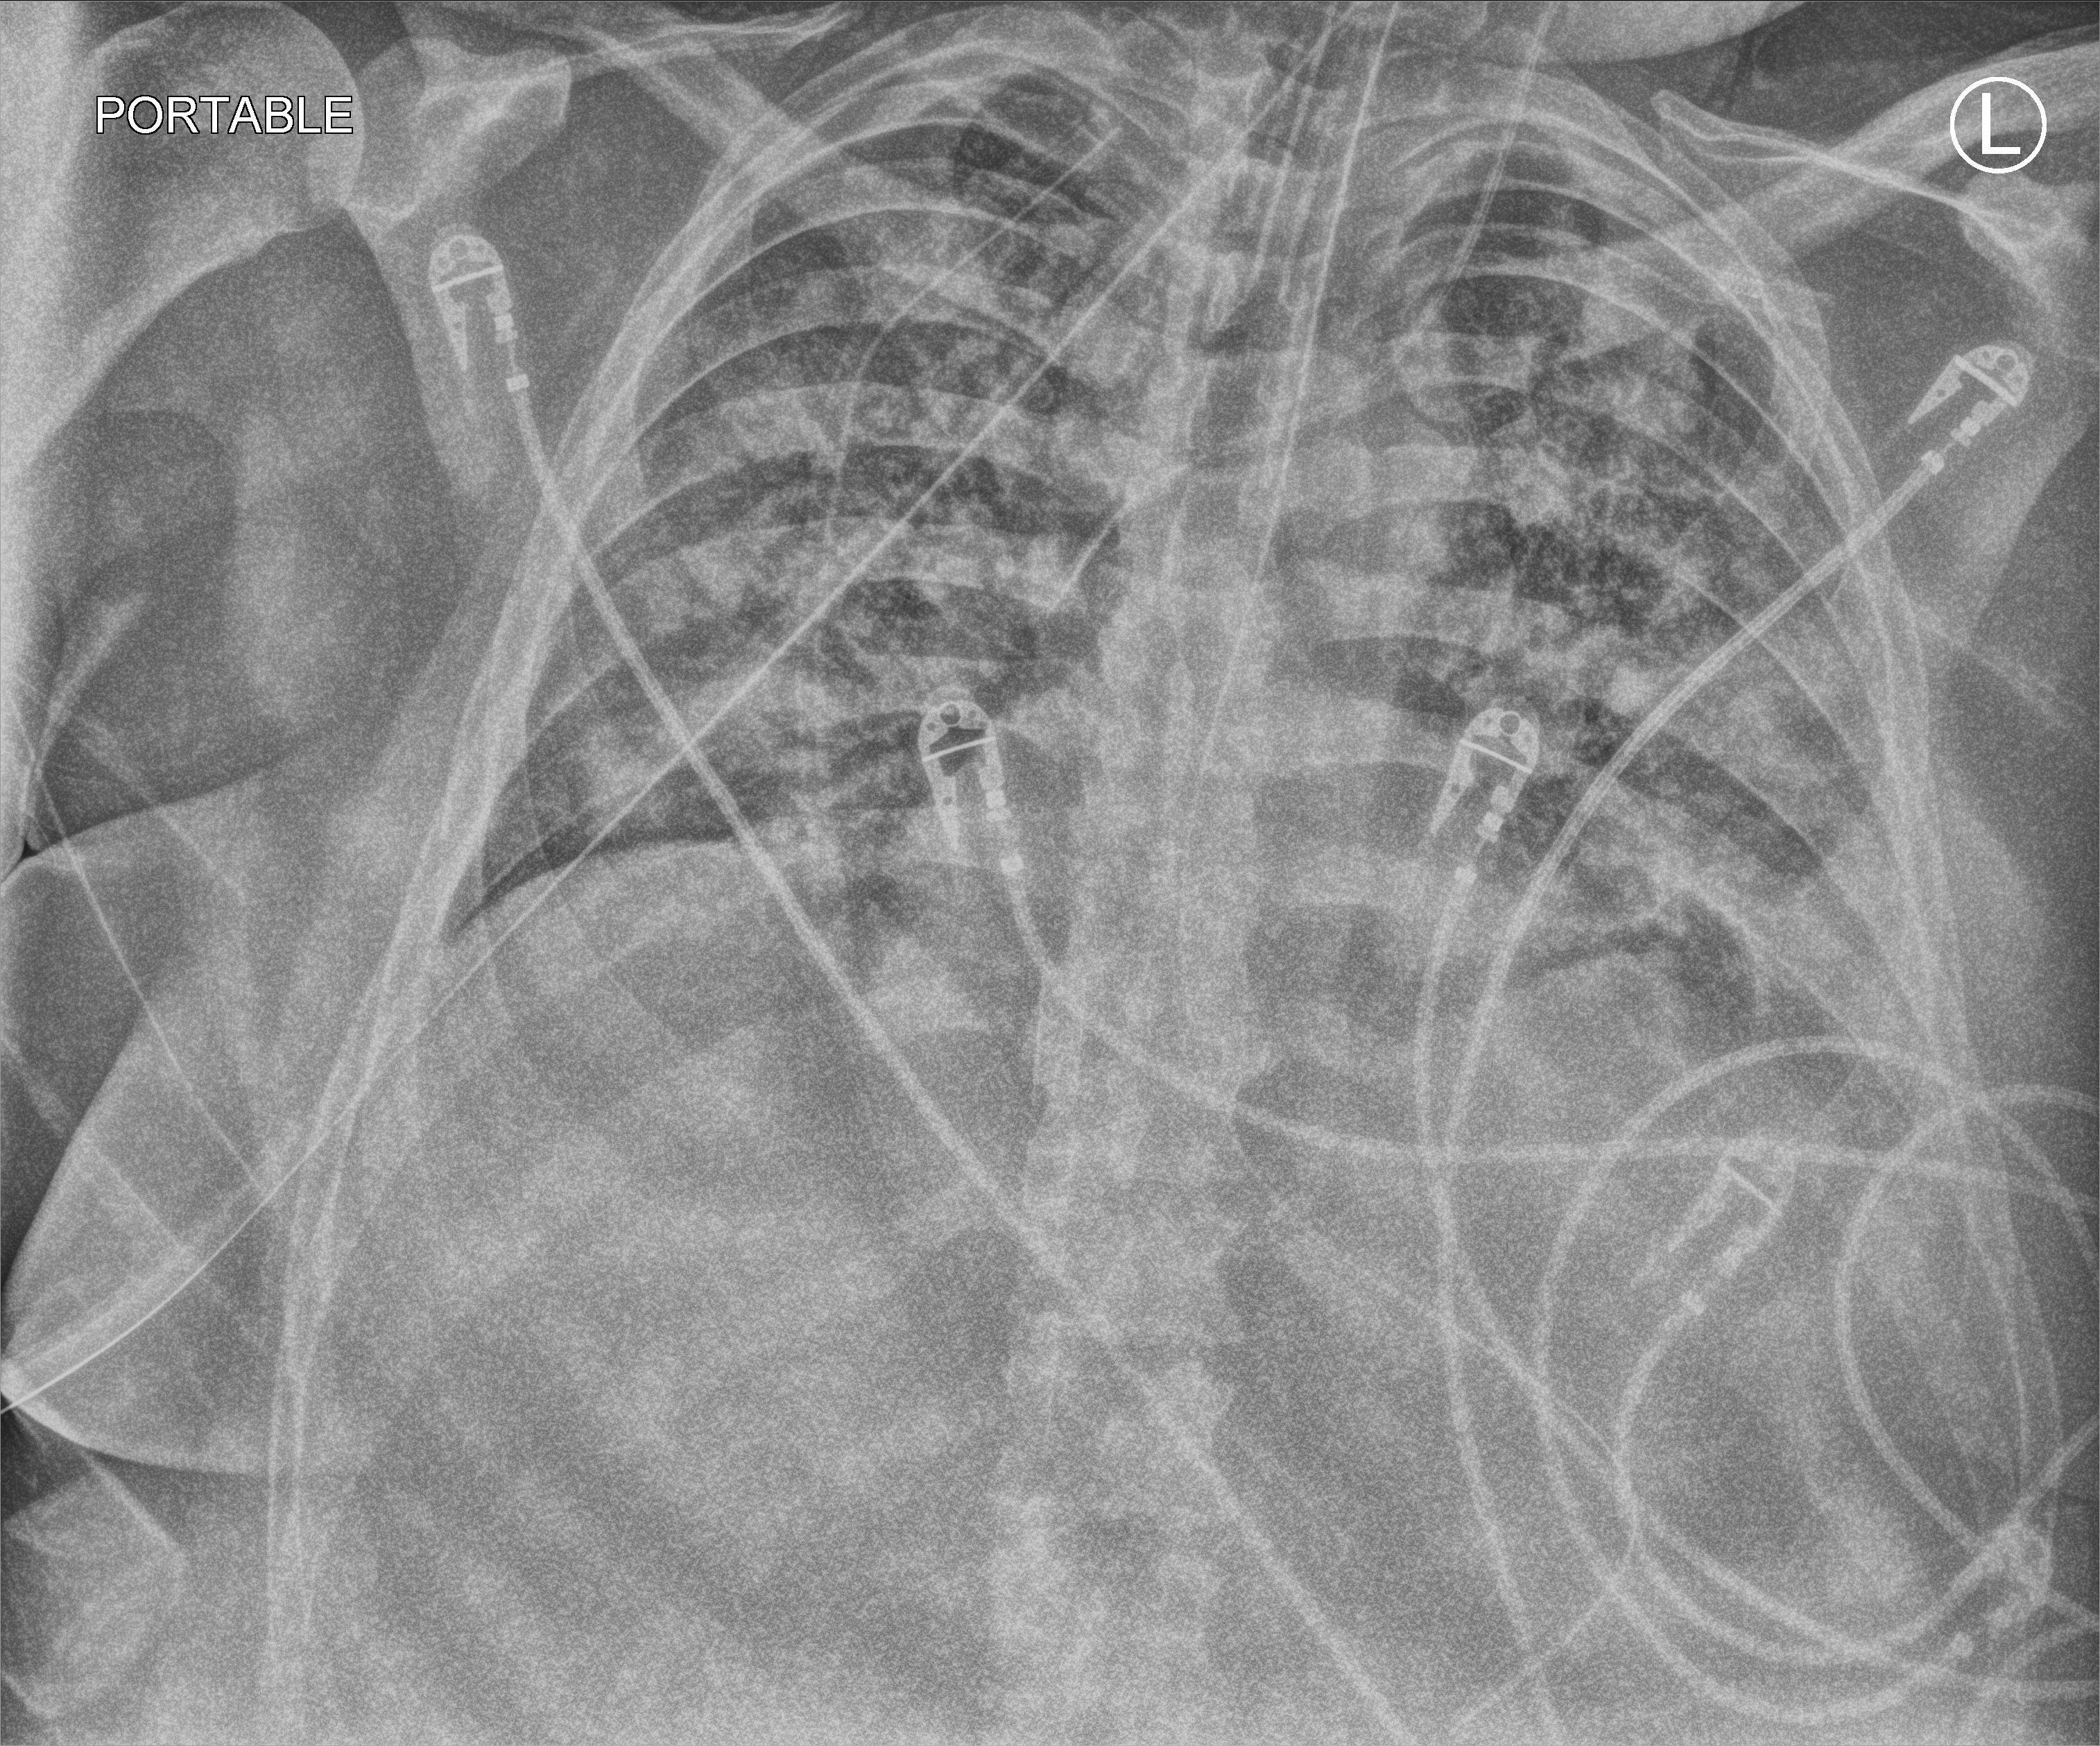
Chest X-ray (portable); anteroposterior (AP) projection. Patient hospitalised with COVID-19, aged 18–59 years.
Hospital-stay facts (about this admission, not read from this image; timing relative to this image not recorded):
- mechanically ventilated during this hospital stay: yes